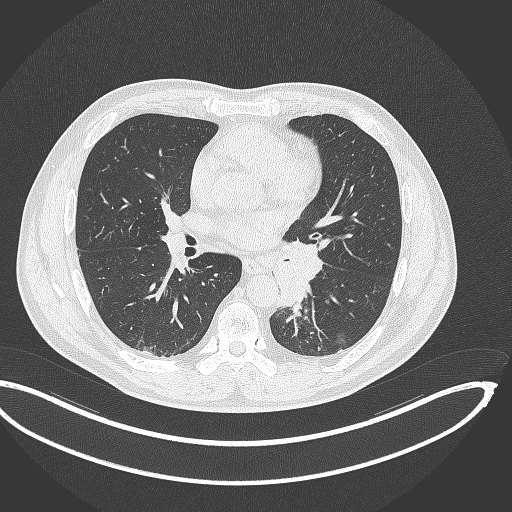
Chest CT, one axial slice. Slice 180 of 362 in the series (ordered by position). Reconstruction kernel B70f. 120 kVp. Lung window (W 1500 / L -600 HU). 1 mm slice thickness. 512 × 512 image matrix, field of view 442 × 442 mm. Male patient, age 50 years. From the clinical record (not read from this slice): clinical TNM (as recorded): T2a N3 M0.
Annotated regions visible in this slice (bounding box drawn by a radiologist):
- lung tumour (recorded histology: squamous cell carcinoma): bounding box <272,239,322,311> (left, top, right, bottom; pixels)